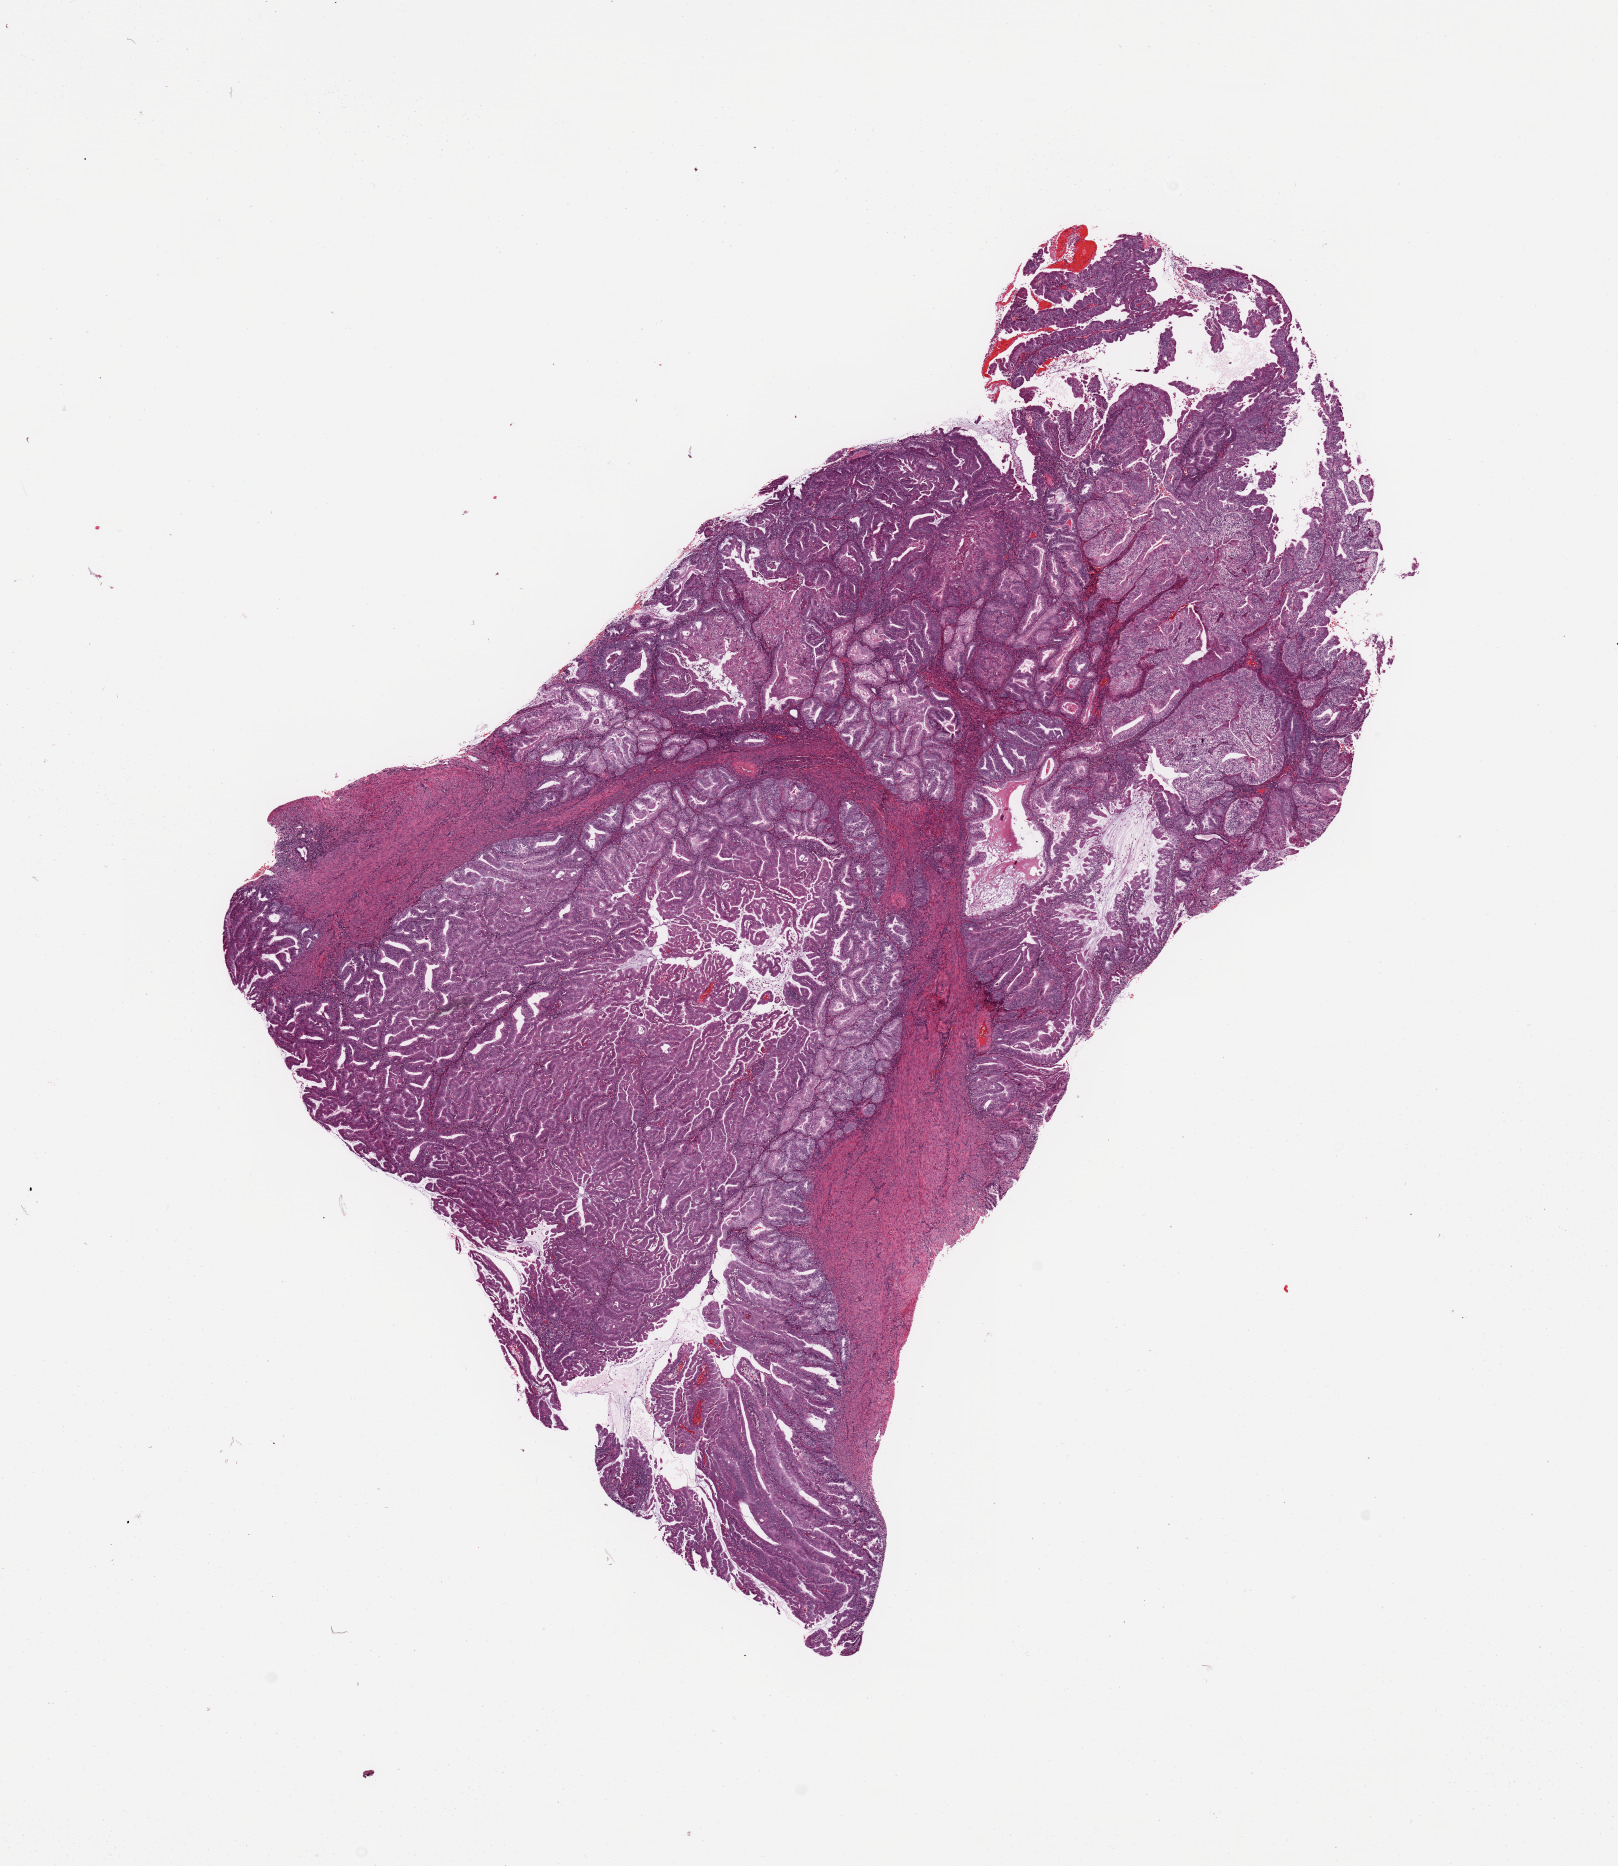
Digitized Hematoxylin and eosin (H&E) stained tissue section (whole slide), a low-resolution overview of the entire scanned area, about 12.8 x 14.8 mm (slide scanned at 20x); tumour tissue sample, sampled site: uterus. Patient: female, age 50 years. Histologic grade: G2 (moderately differentiated). Pathologist review of this section (percent, as recorded): tumour nuclei 90%, necrosis 0%.
Diagnosis: Endometrioid adenocarcinoma, NOS. AJCC pathologic stage: I.